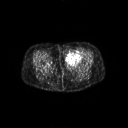
FDG PET of an extremity soft-tissue mass (from a PET/CT study), one axial slice. Slice 26 of 267 in the series (ordered by position). 128 × 128 image matrix, field of view 700 × 700 mm. Patient: female, 47 years. Case-level facts recorded for this patient, not image findings: histological type: myxofibrosarcoma; grade: intermediate; site of the primary tumour: left thigh.
Structures marked on this image (expert contour drawn on MRI and transferred to this co-registered scan by the dataset authors):
- gross tumour volume including surrounding oedema: box from (x=65, y=51) to (x=82, y=64) px
- gross tumour volume (mass): (x=66, y=52)–(x=82, y=64)